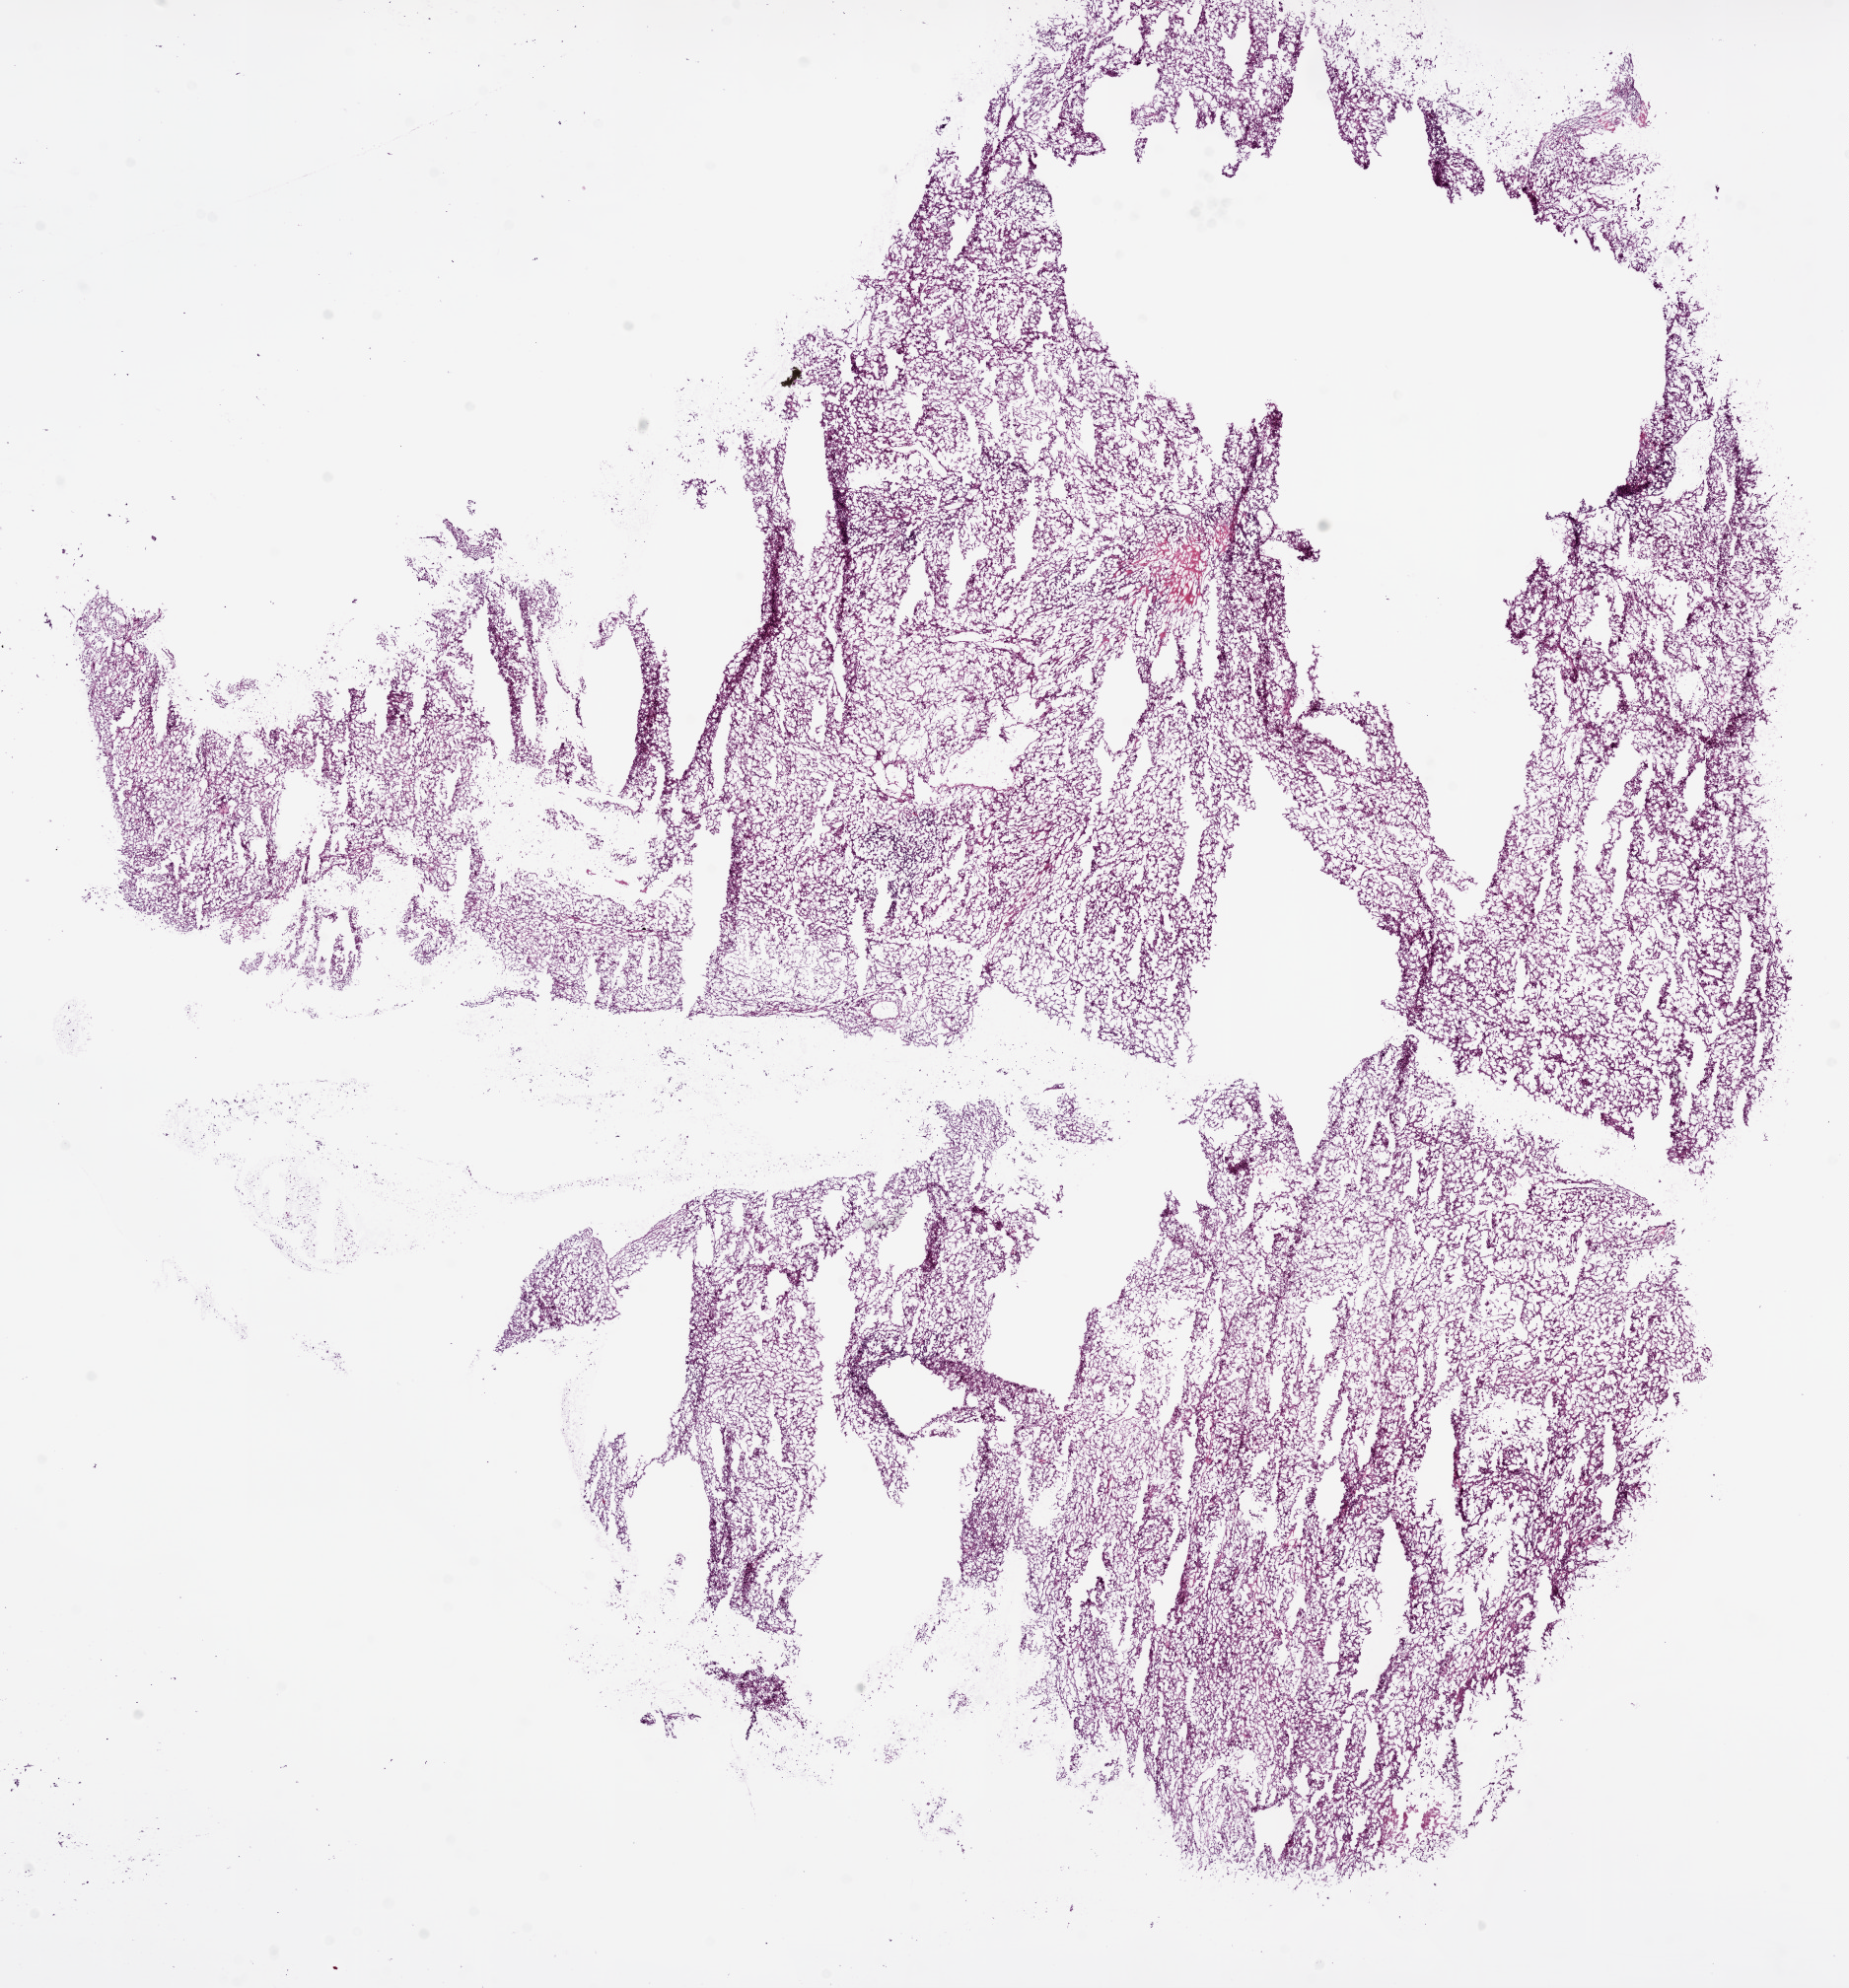
Whole-slide histology image, H&E-stained, low-resolution overview of the scanned area, about 15.0 x 16.2 mm. Frozen section from the bottom of the tissue portion. Primary tumour sample from the kidney. Female, age 73 years at initial diagnosis. Histologic grade: G4 (undifferentiated). Pathologist review of this section (percent, as recorded): tumour cells 95%, tumour nuclei 90%, normal cells 0%, stromal cells 5%, necrosis 0%.
TNM: T3a N0 M0. AJCC pathologic stage: III. Laterality: right. Pathologic diagnosis: Clear cell adenocarcinoma, NOS.